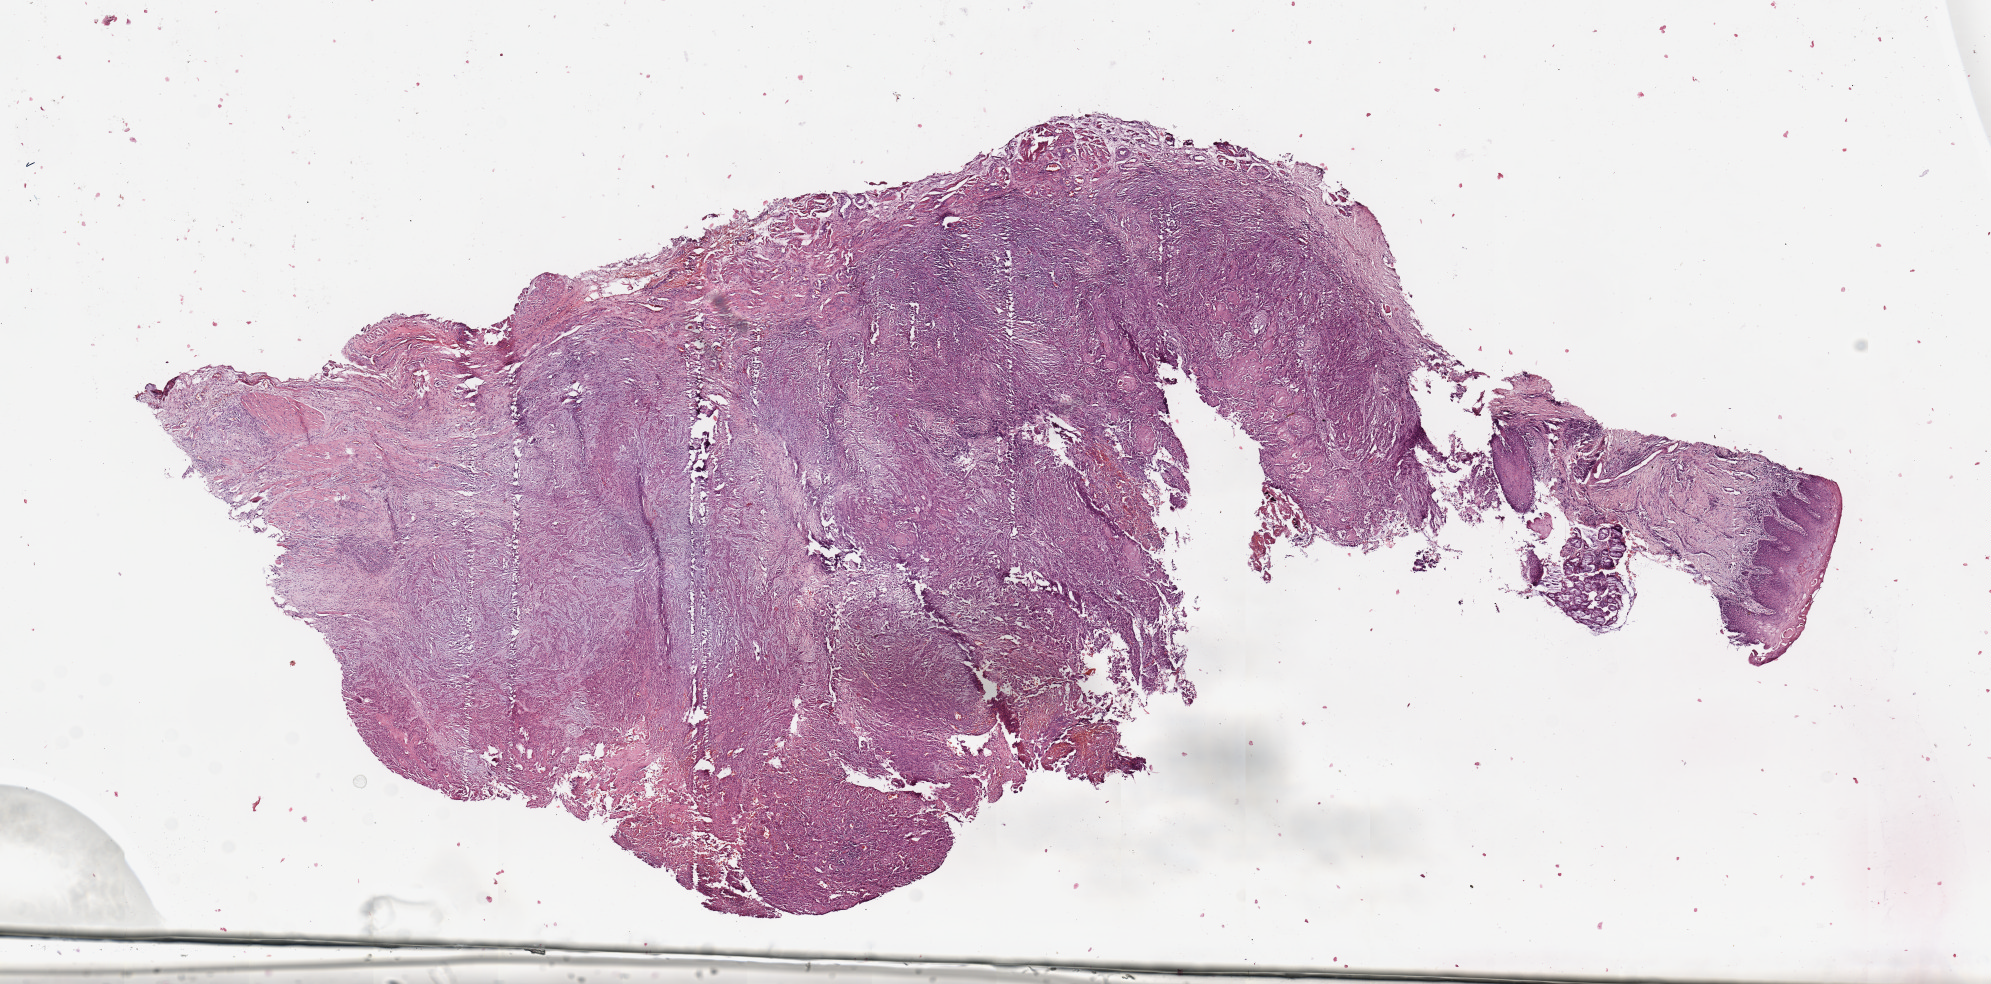
Whole-slide histology image, H&E-stained, whole scanned area (about 15.8 x 7.8 mm, slide scanned at 20x) shown as a low-resolution overview, tumour tissue sample, sampled site: oropharynx. Male, 51 y/o. Histologic grade: G2 (moderately differentiated). Pathologist review of this section (percent, as recorded): tumour nuclei 80%, necrosis 5%.
AJCC pathologic stage: III. Primary tumour site (as recorded): oropharynx. Diagnosis: Squamous cell carcinoma, NOS (oropharynx, NOS).